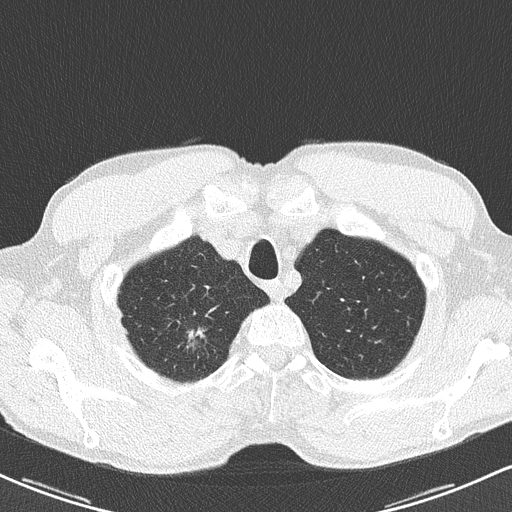
Axial slice from a low-dose chest CT screening exam. Baseline screening round. Lung window (W 1500 / L -600 HU). 2 mm slice thickness. Lung (sharp) reconstruction kernel (B50f). Slice 29 of 211 in the series. Male, age 62 years at enrolment. Former smoker at enrolment.
Lesion marked by an expert reader, box from (x=167, y=324) to (x=218, y=371) px. Reader record for this screening exam (exam-level; its link to the box is not recorded): non-calcified nodule or mass ≥4 mm, right upper lobe, 12 × 9 mm, spiculated (stellate) margins, soft tissue attenuation. Official screen result: positive, change unspecified: nodule(s) >= 4 mm or enlarging nodule(s), mass(es), or other non-specific abnormalities suspicious for lung cancer. Later outcome: lung cancer diagnosed 398 days after this screen (after the second annual screen) — bronchiolo-alveolar adenocarcinoma, NOS, right upper lobe, well differentiated (G1), stage IA (AJCC 6th edition), 15 mm at pathology.